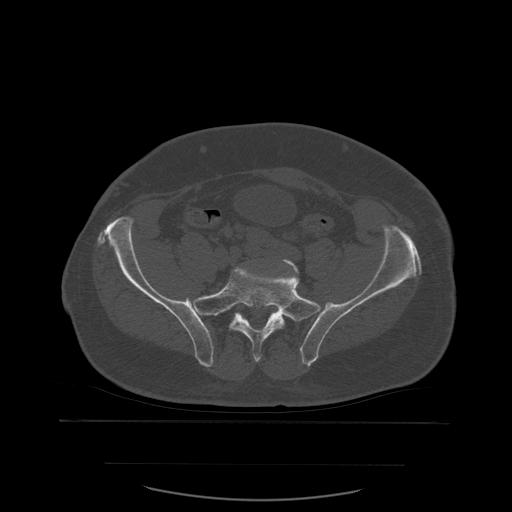
CT including the spine, one axial slice. Position 116 of 590 along the scan axis. Bone window (W 1800 / L 400 HU). 512 × 512 image matrix, field of view 479 × 479 mm. Patient age 71 years. From the clinical record (not read from this slice): primary cancer: lung; vertebrae with lytic lesions (as recorded): T1, T2, L5, S1.
Structures marked on this image (semi-automatically segmented with operator editing):
- L5 vertebra: bounding box <254,259,299,357> (left, top, right, bottom; pixels)